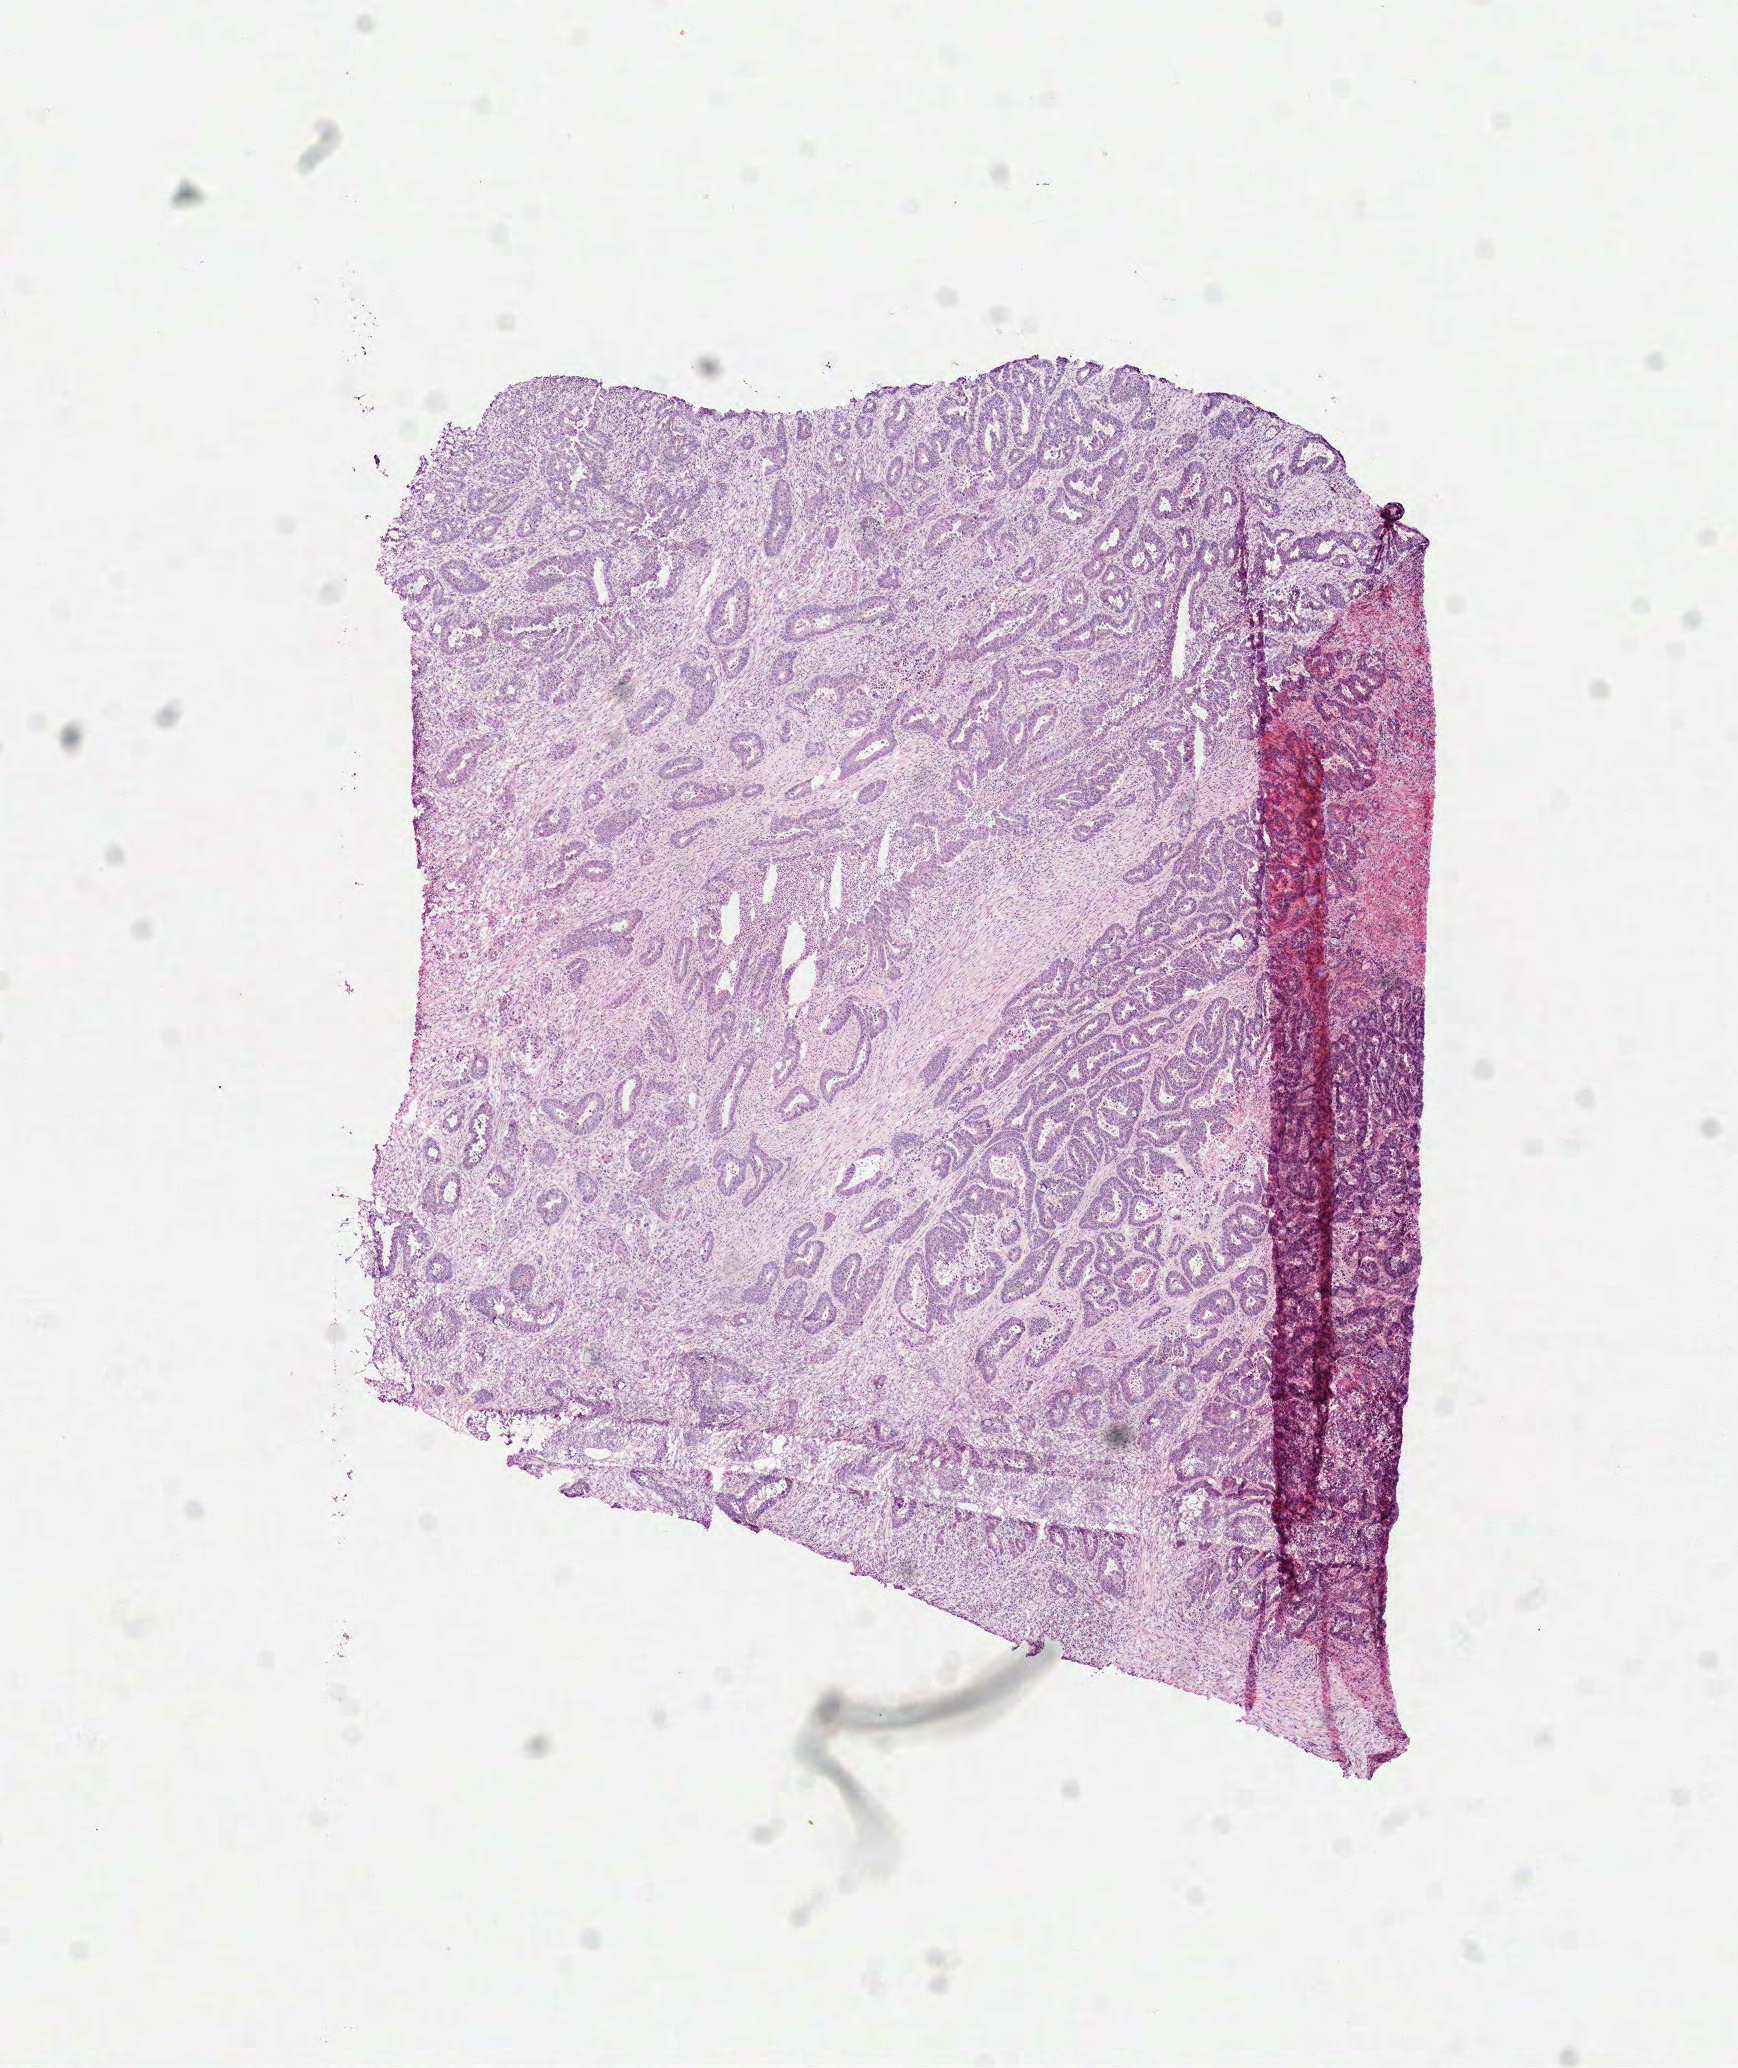
Whole-slide histology image, Hematoxylin and eosin (H&E) stained, shown as a low-resolution overview of the whole scanned area (about 7.0 x 8.3 mm); frozen section; primary tumour sample from the colon. Male, age 65 years at initial diagnosis. Composition of this section per pathologist review: tumour cells 60%, tumour nuclei 75%, normal cells 0%, stromal cells 33%, necrosis 7%. Infiltration values recorded for this section: lymphocyte infiltration 5%, monocyte infiltration 0%, neutrophil infiltration 1%.
Lymph nodes positive (case pathology): 3 of 34 examined. AJCC pathologic stage: IIIB (7th edition). Pathologic diagnosis: Adenocarcinoma, NOS (sigmoid colon).